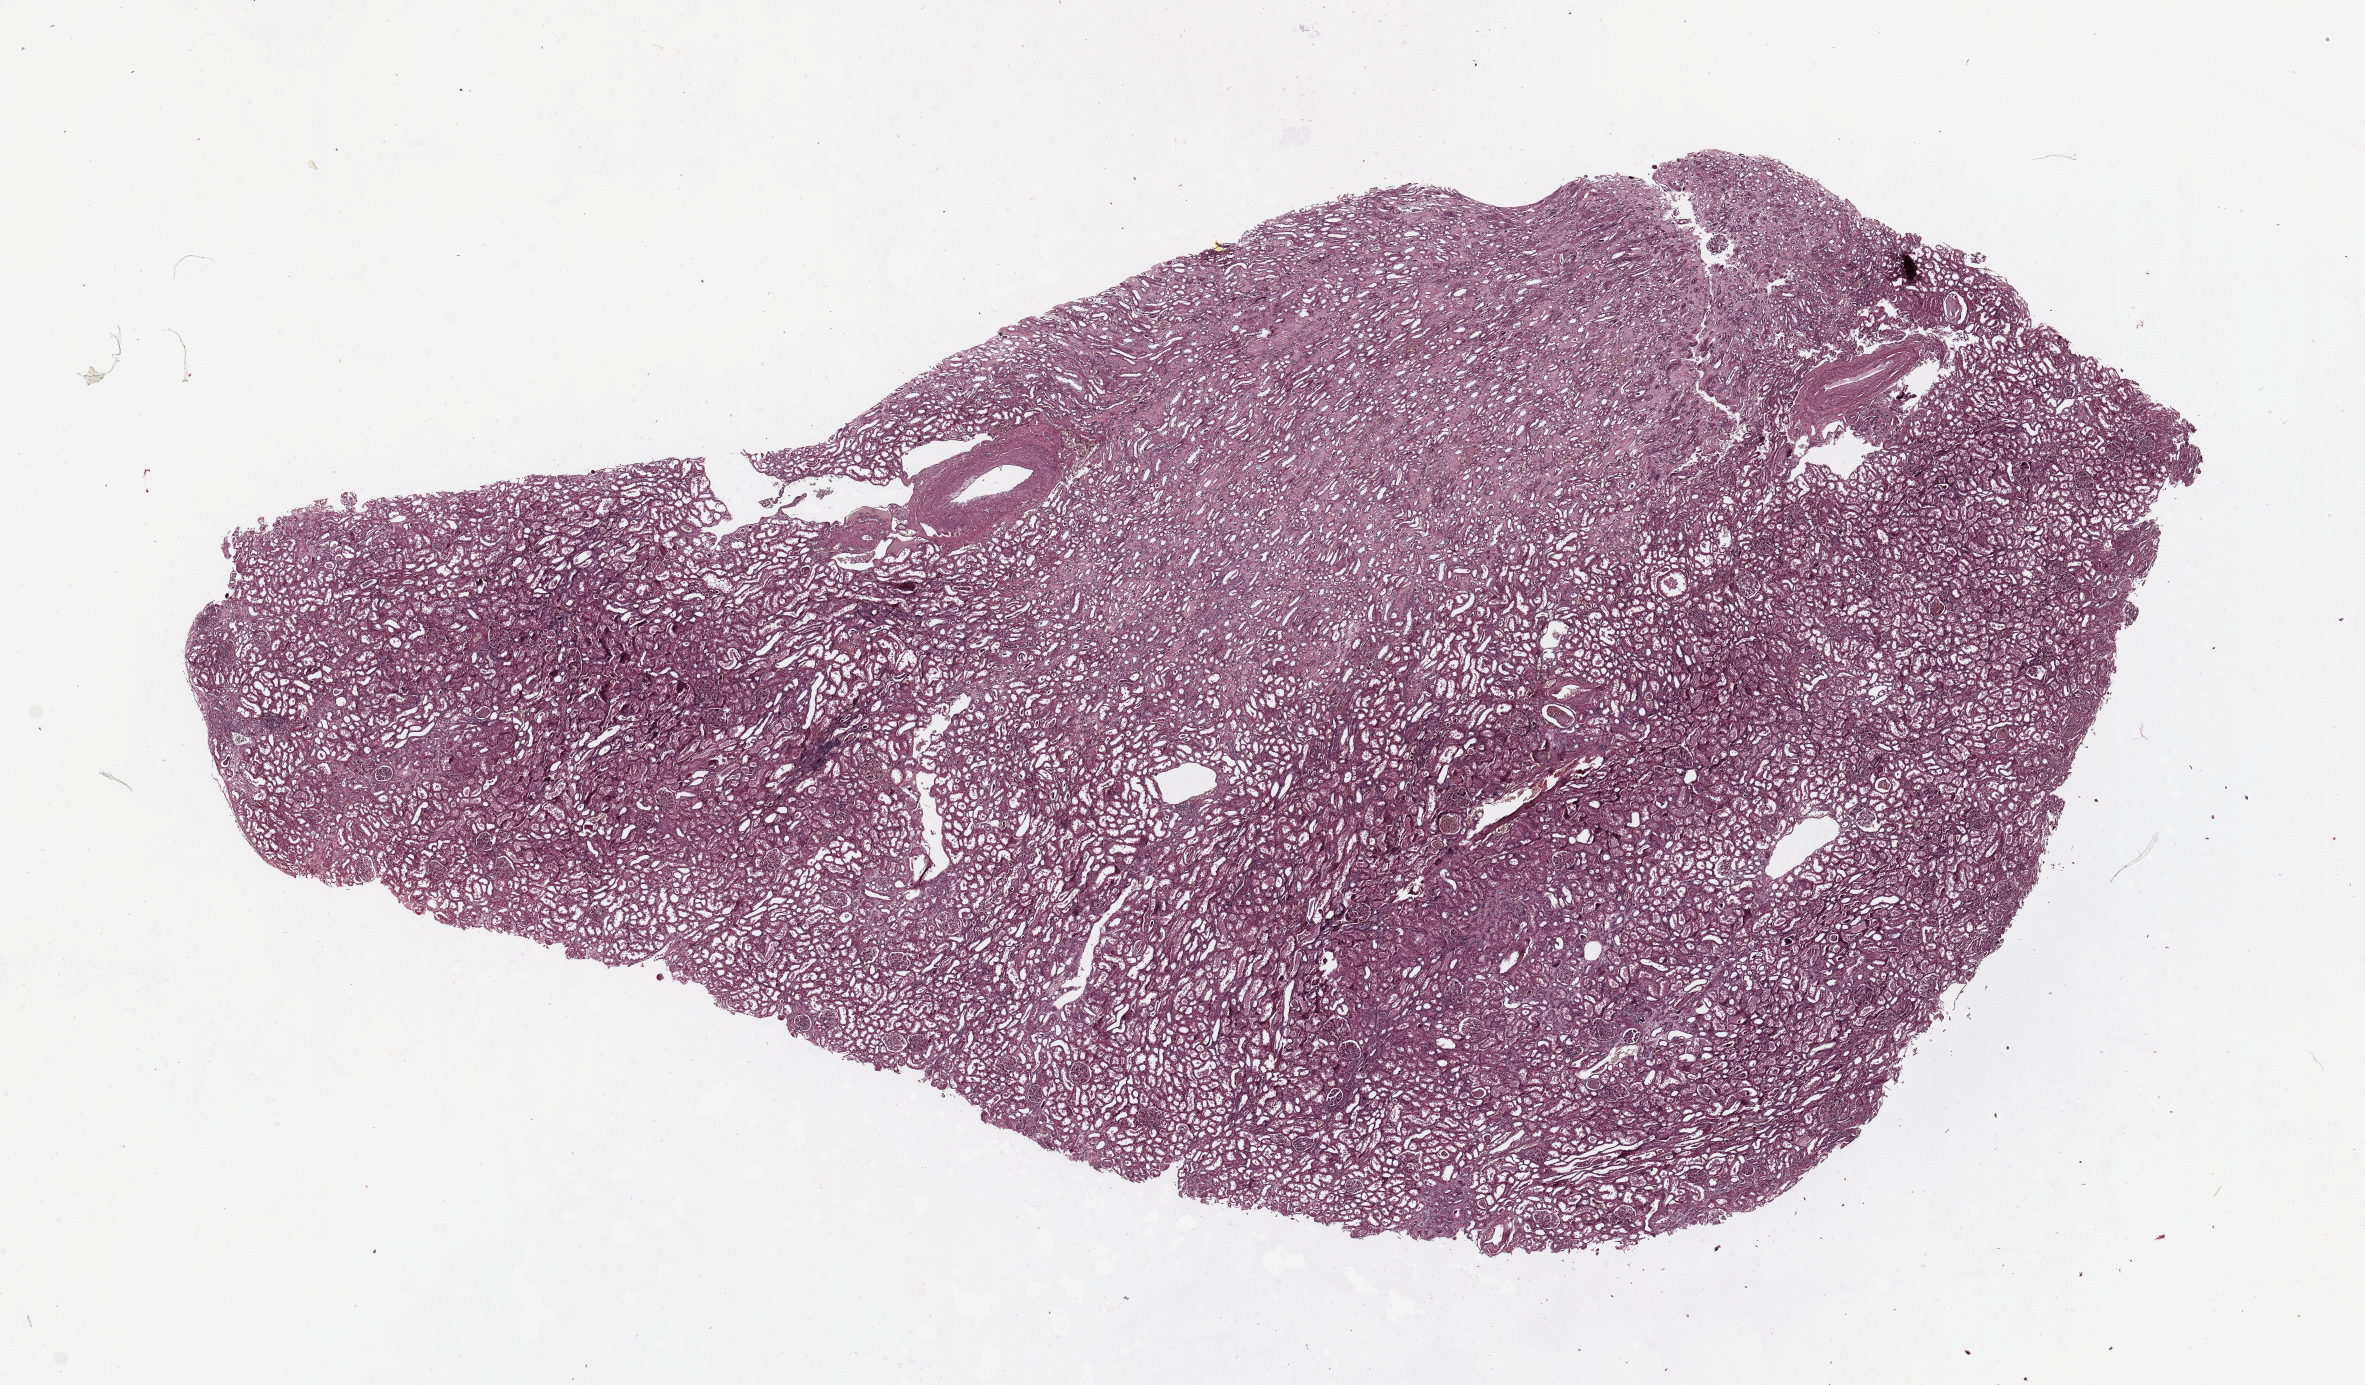
Digitized Hematoxylin and eosin (H&E) stained tissue section (whole slide) — a low-resolution overview of the entire scanned area, about 18.7 x 11.0 mm (from a 20x scan). Normal (non-tumour) tissue sample, sampled site: kidney. Male, 67 y/o.
• this section: normal (non-tumour) tissue from the same patient
• patient diagnosis: Renal cell carcinoma, NOS